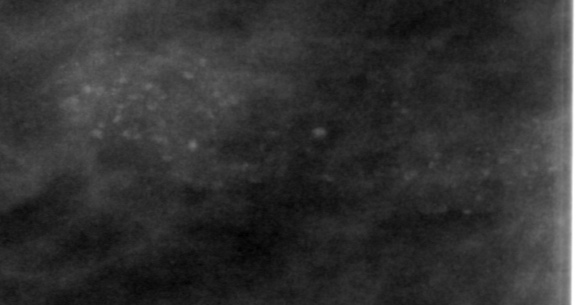
Crop from a digitized film mammogram around one marked abnormality; left breast; MLO view; BI-RADS breast density category 1 (scale 1–4).
- Finding: calcifications, morphology pleomorphic, distribution clustered; BI-RADS assessment category 4; pathology result (as recorded, not read from the image): benign.